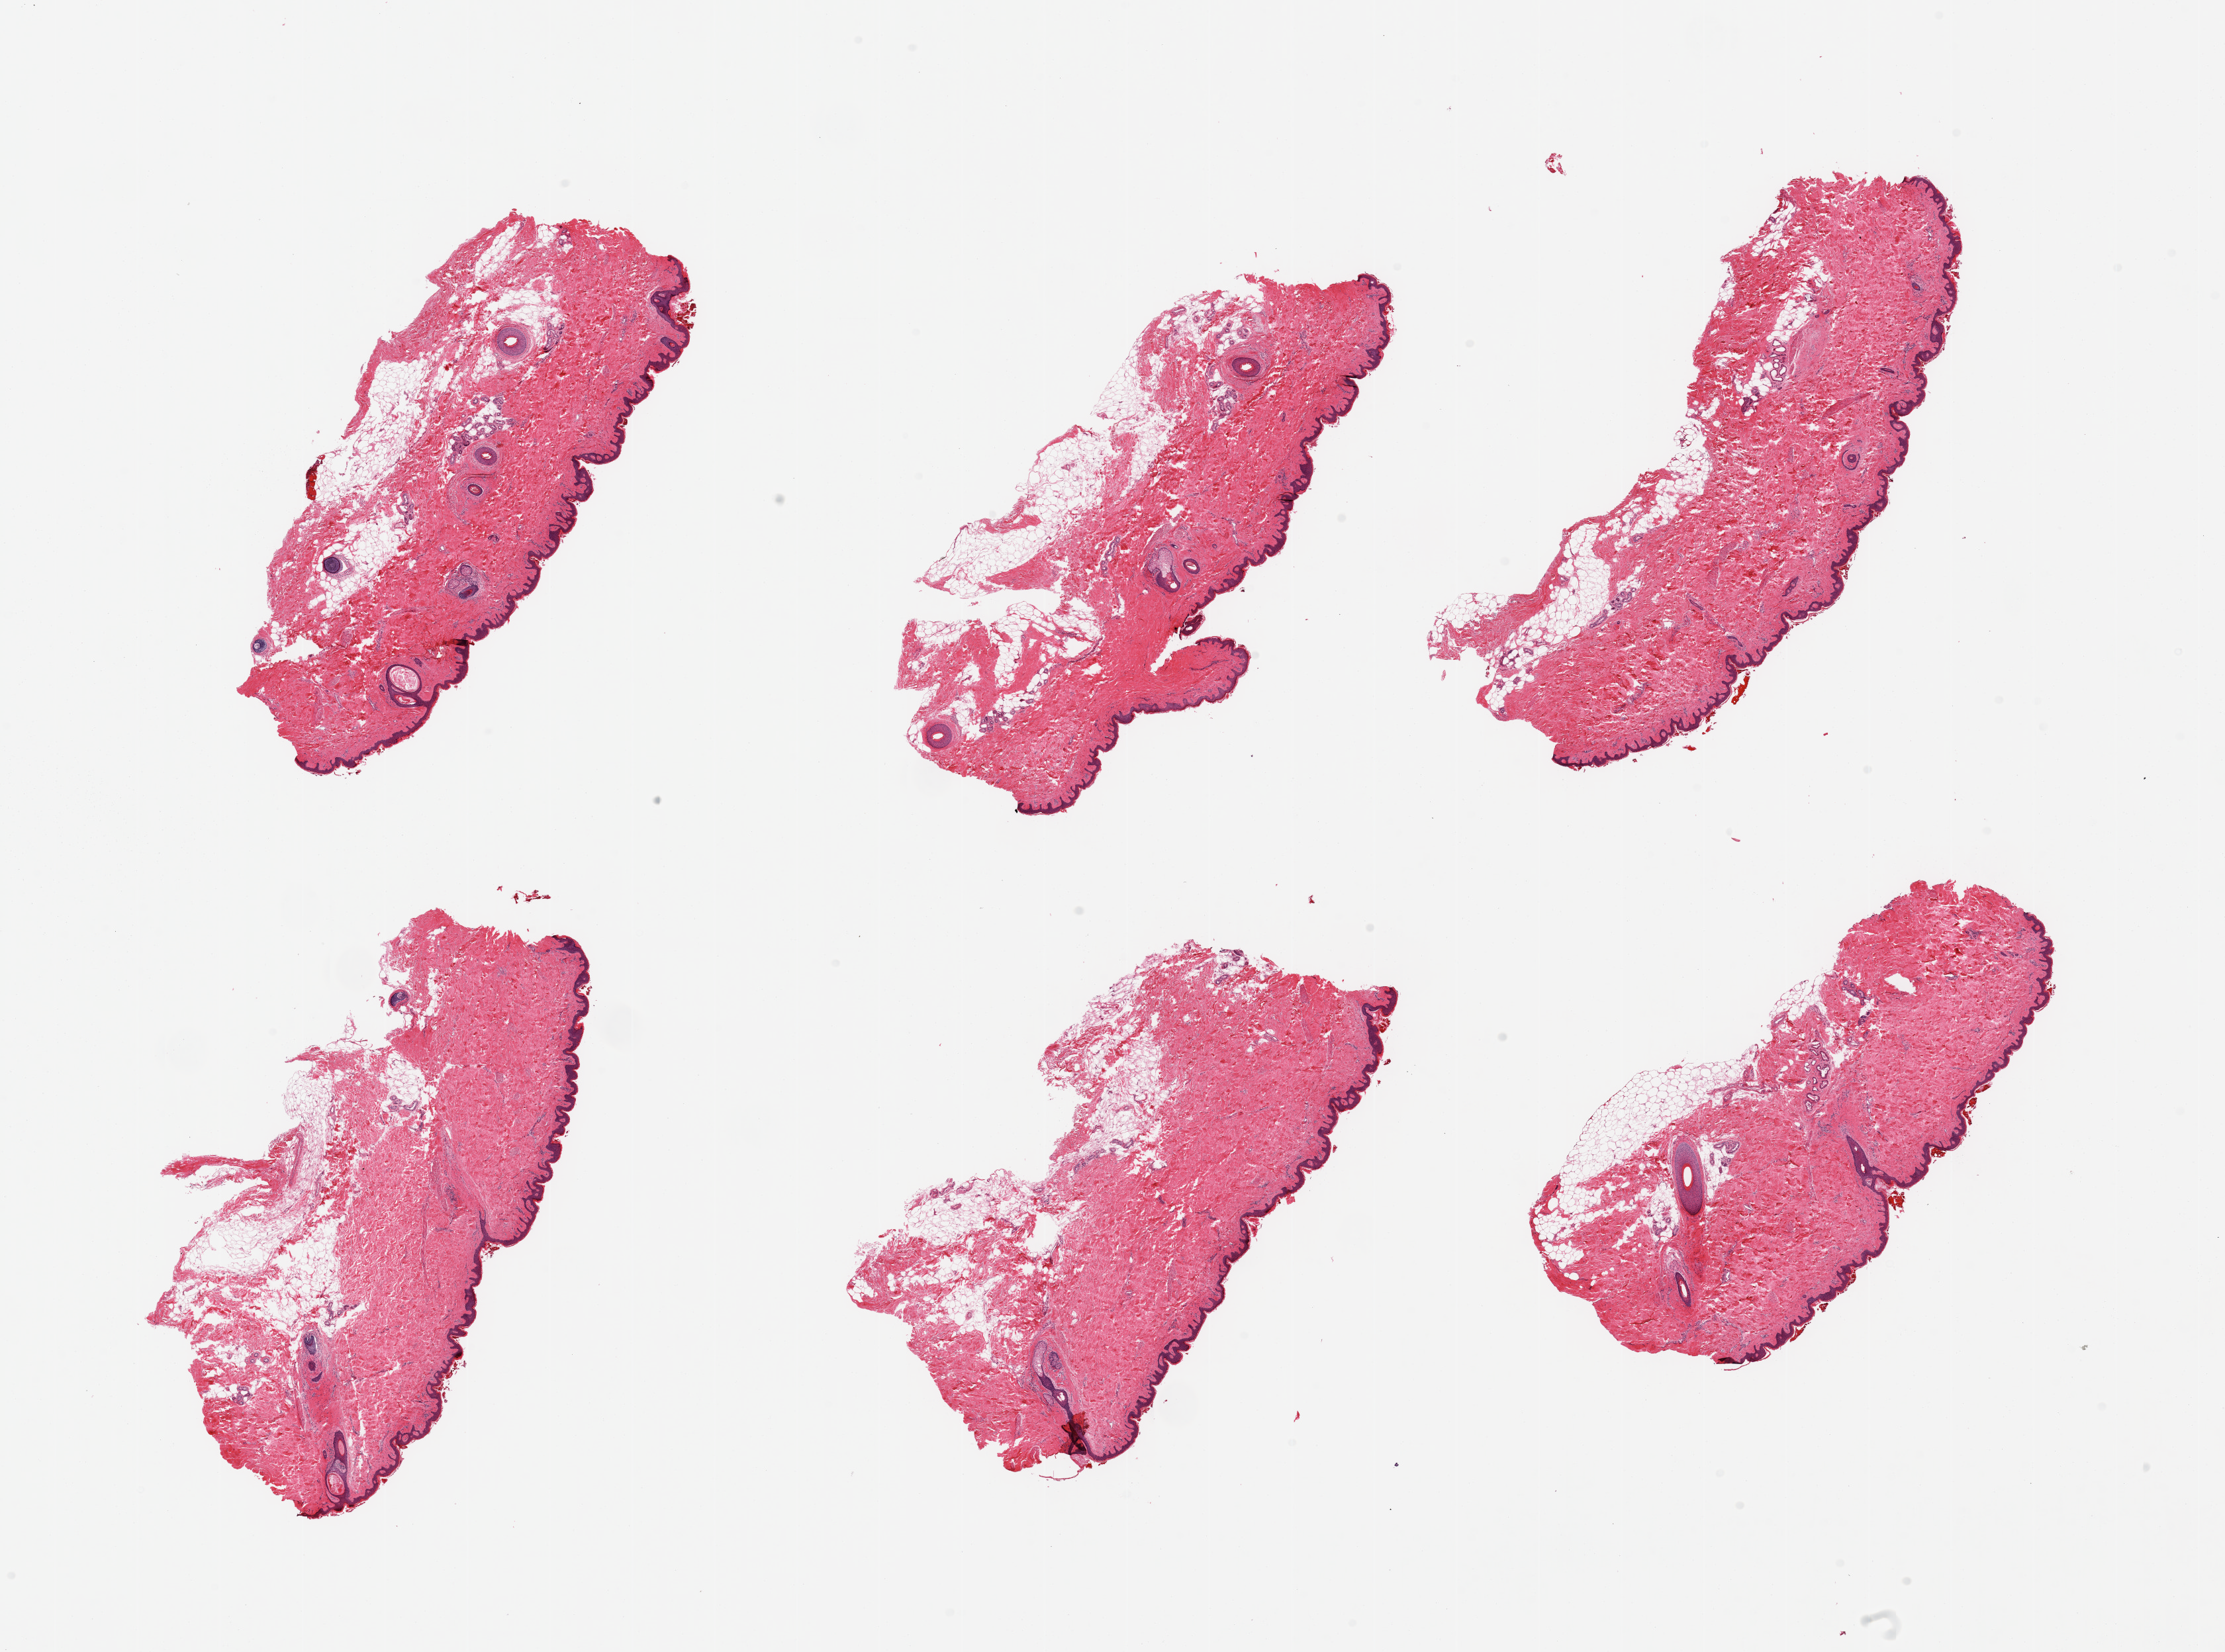
Haematoxylin and eosin whole-slide image, whole scanned area (about 26.6 x 19.7 mm, slide scanned at 20x) shown as a low-resolution overview. PAXgene-fixed paraffin-embedded (PFPE) section. Section of skin of suprapubic region (target tissue). Tissue donor sample.
Pathologist's review note for this sample: 6 pieces, adherent dermal fat up to ~1mm; squamous epithelium is ~40-50 microns.